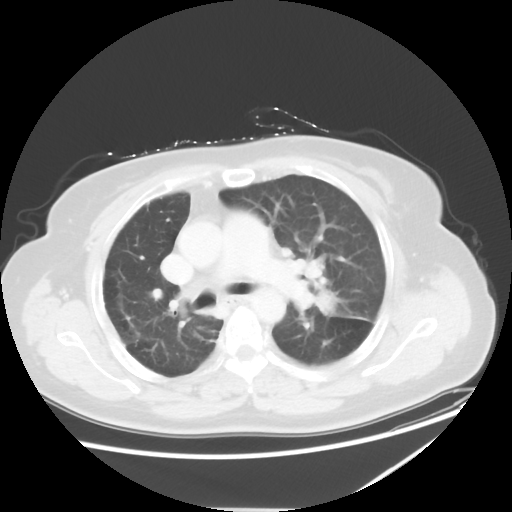
Chest CT, one axial slice; slice 36 of 54 in the series (ordered by position); reconstruction kernel STANDARD; 120 kVp; lung window (W 1500 / L -600 HU); 5 mm slice thickness; 512 × 512 image matrix. Patient: female, 61 years. Case-level facts recorded for this patient, not image findings: clinical TNM (as recorded): T1c N3 M1.
Outlined on this slice (rectangle marked by the reading radiologist):
- lung tumour (recorded histology: adenocarcinoma): box from (x=312, y=283) to (x=381, y=327) px